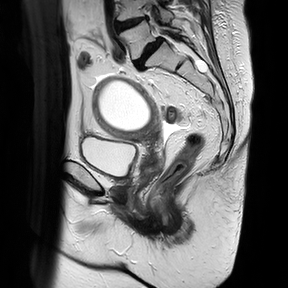
Pelvic MRI for cervical cancer, one sagittal slice. Slice 19 of 30 in the series (ordered by position). T2-weighted. 1.5 T. TE 100 ms, TR 4816.3 ms. 4 mm slice thickness. 288 × 288 image matrix. Patient: female, 74 years.
Outlined on this slice (outlined manually by an expert reader):
- uterus and cervix: box from (x=91, y=75) to (x=161, y=187) px